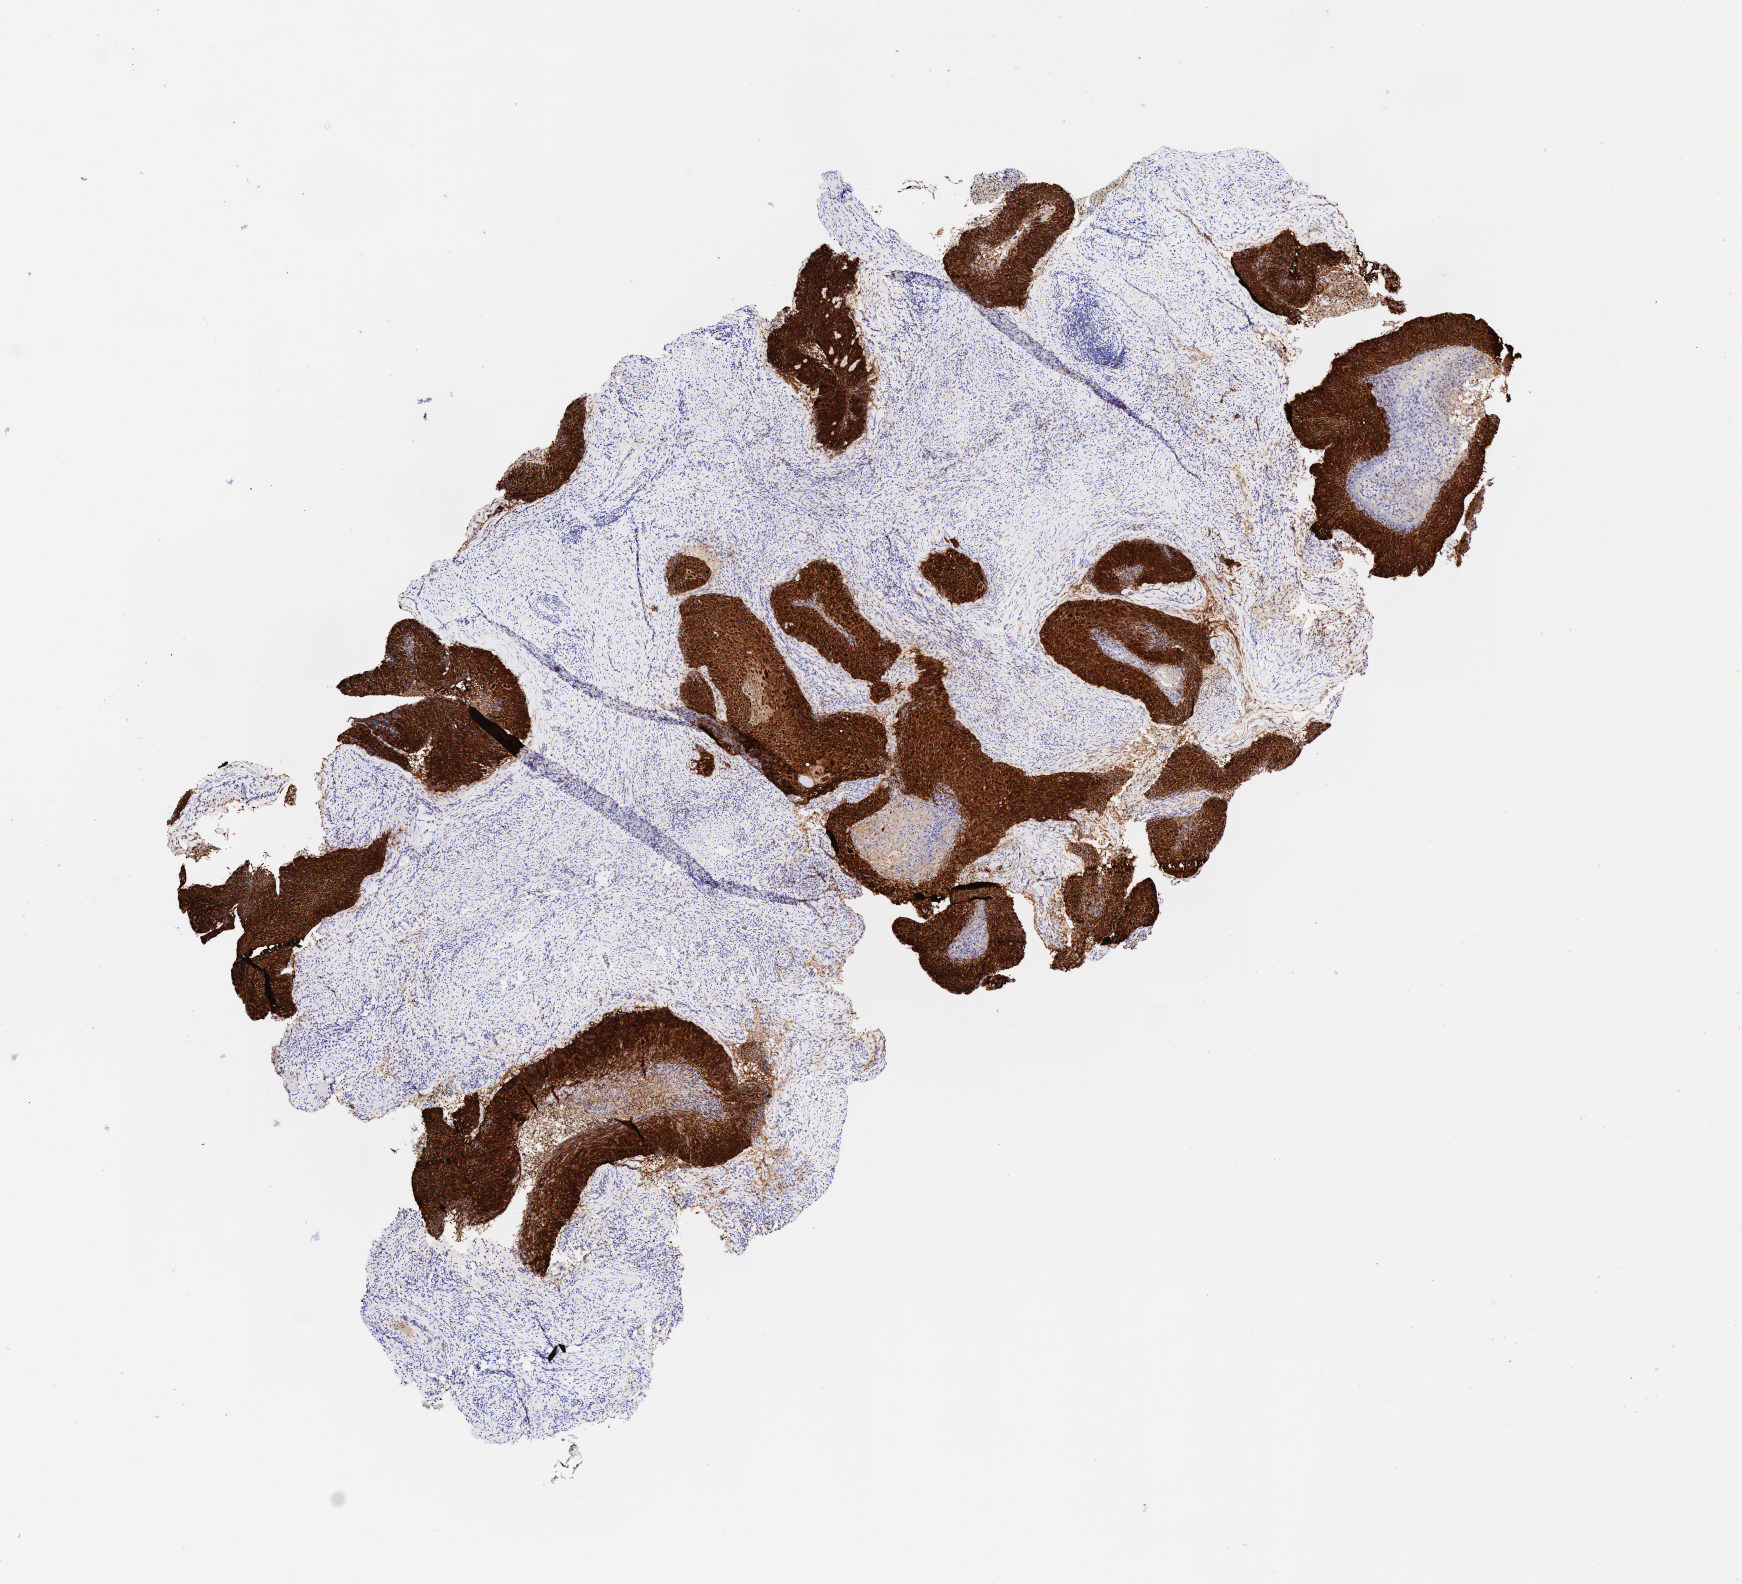
Whole-slide image, immunohistochemical stain for p16 (p16INK4a), shown as a low-resolution overview of the whole scanned area (about 7.0 x 6.4 mm); tumor tissue; anatomic site: cervix. Patient female; age 54 years.
Diagnosis: Squamous cell carcinoma, large cell, nonkeratinizing, NOS.